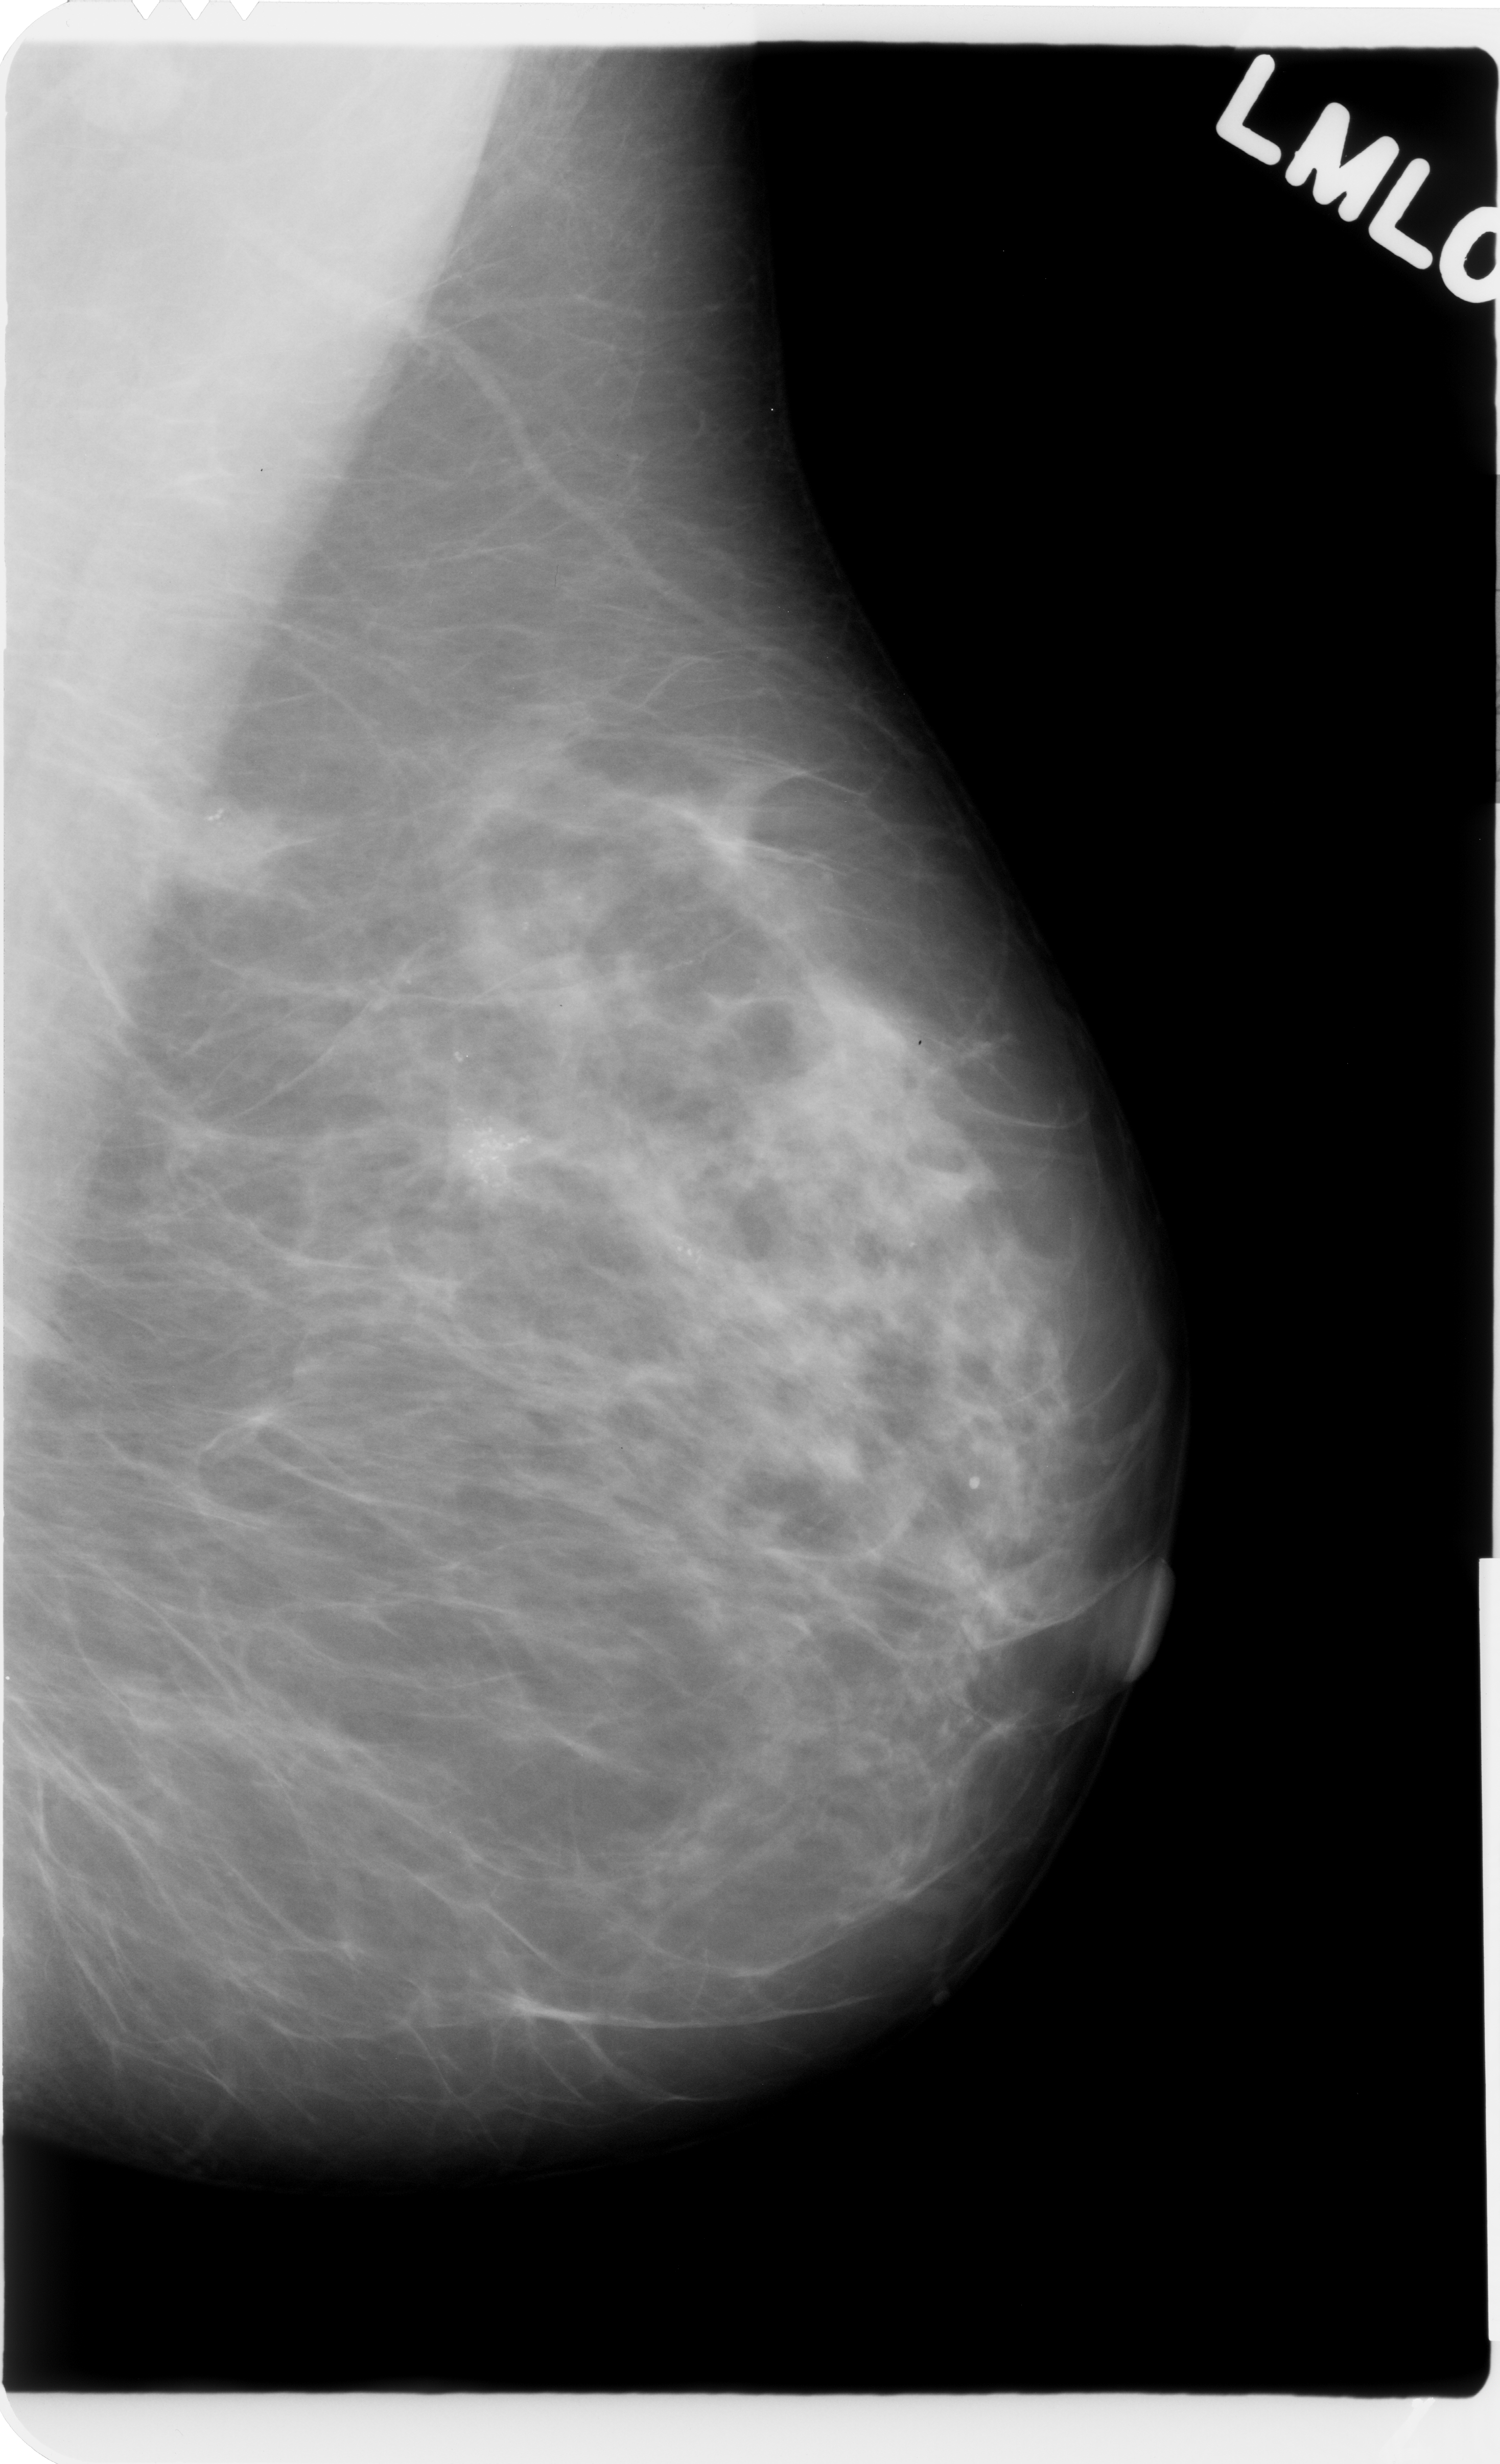
Scanned film-screen mammogram; left breast; mediolateral oblique (MLO) view; breast composition: scattered fibroglandular densities (BI-RADS density category 2 of 4).
Abnormality record for this image: Finding 1 of 3: calcifications, morphology pleomorphic, distribution clustered; BI-RADS assessment category 5; pathology result (as recorded, not read from the image): malignant. Finding 2 of 3: calcifications, morphology pleomorphic, distribution clustered; BI-RADS assessment category 5; subtlety rating 5 on a 1 (subtle) to 5 (obvious) scale; pathology (as recorded): malignant. Finding 3 of 3: calcifications, morphology pleomorphic, distribution clustered; BI-RADS assessment category 5; subtlety rating 5 on a 1 (subtle) to 5 (obvious) scale; pathology (as recorded): malignant.